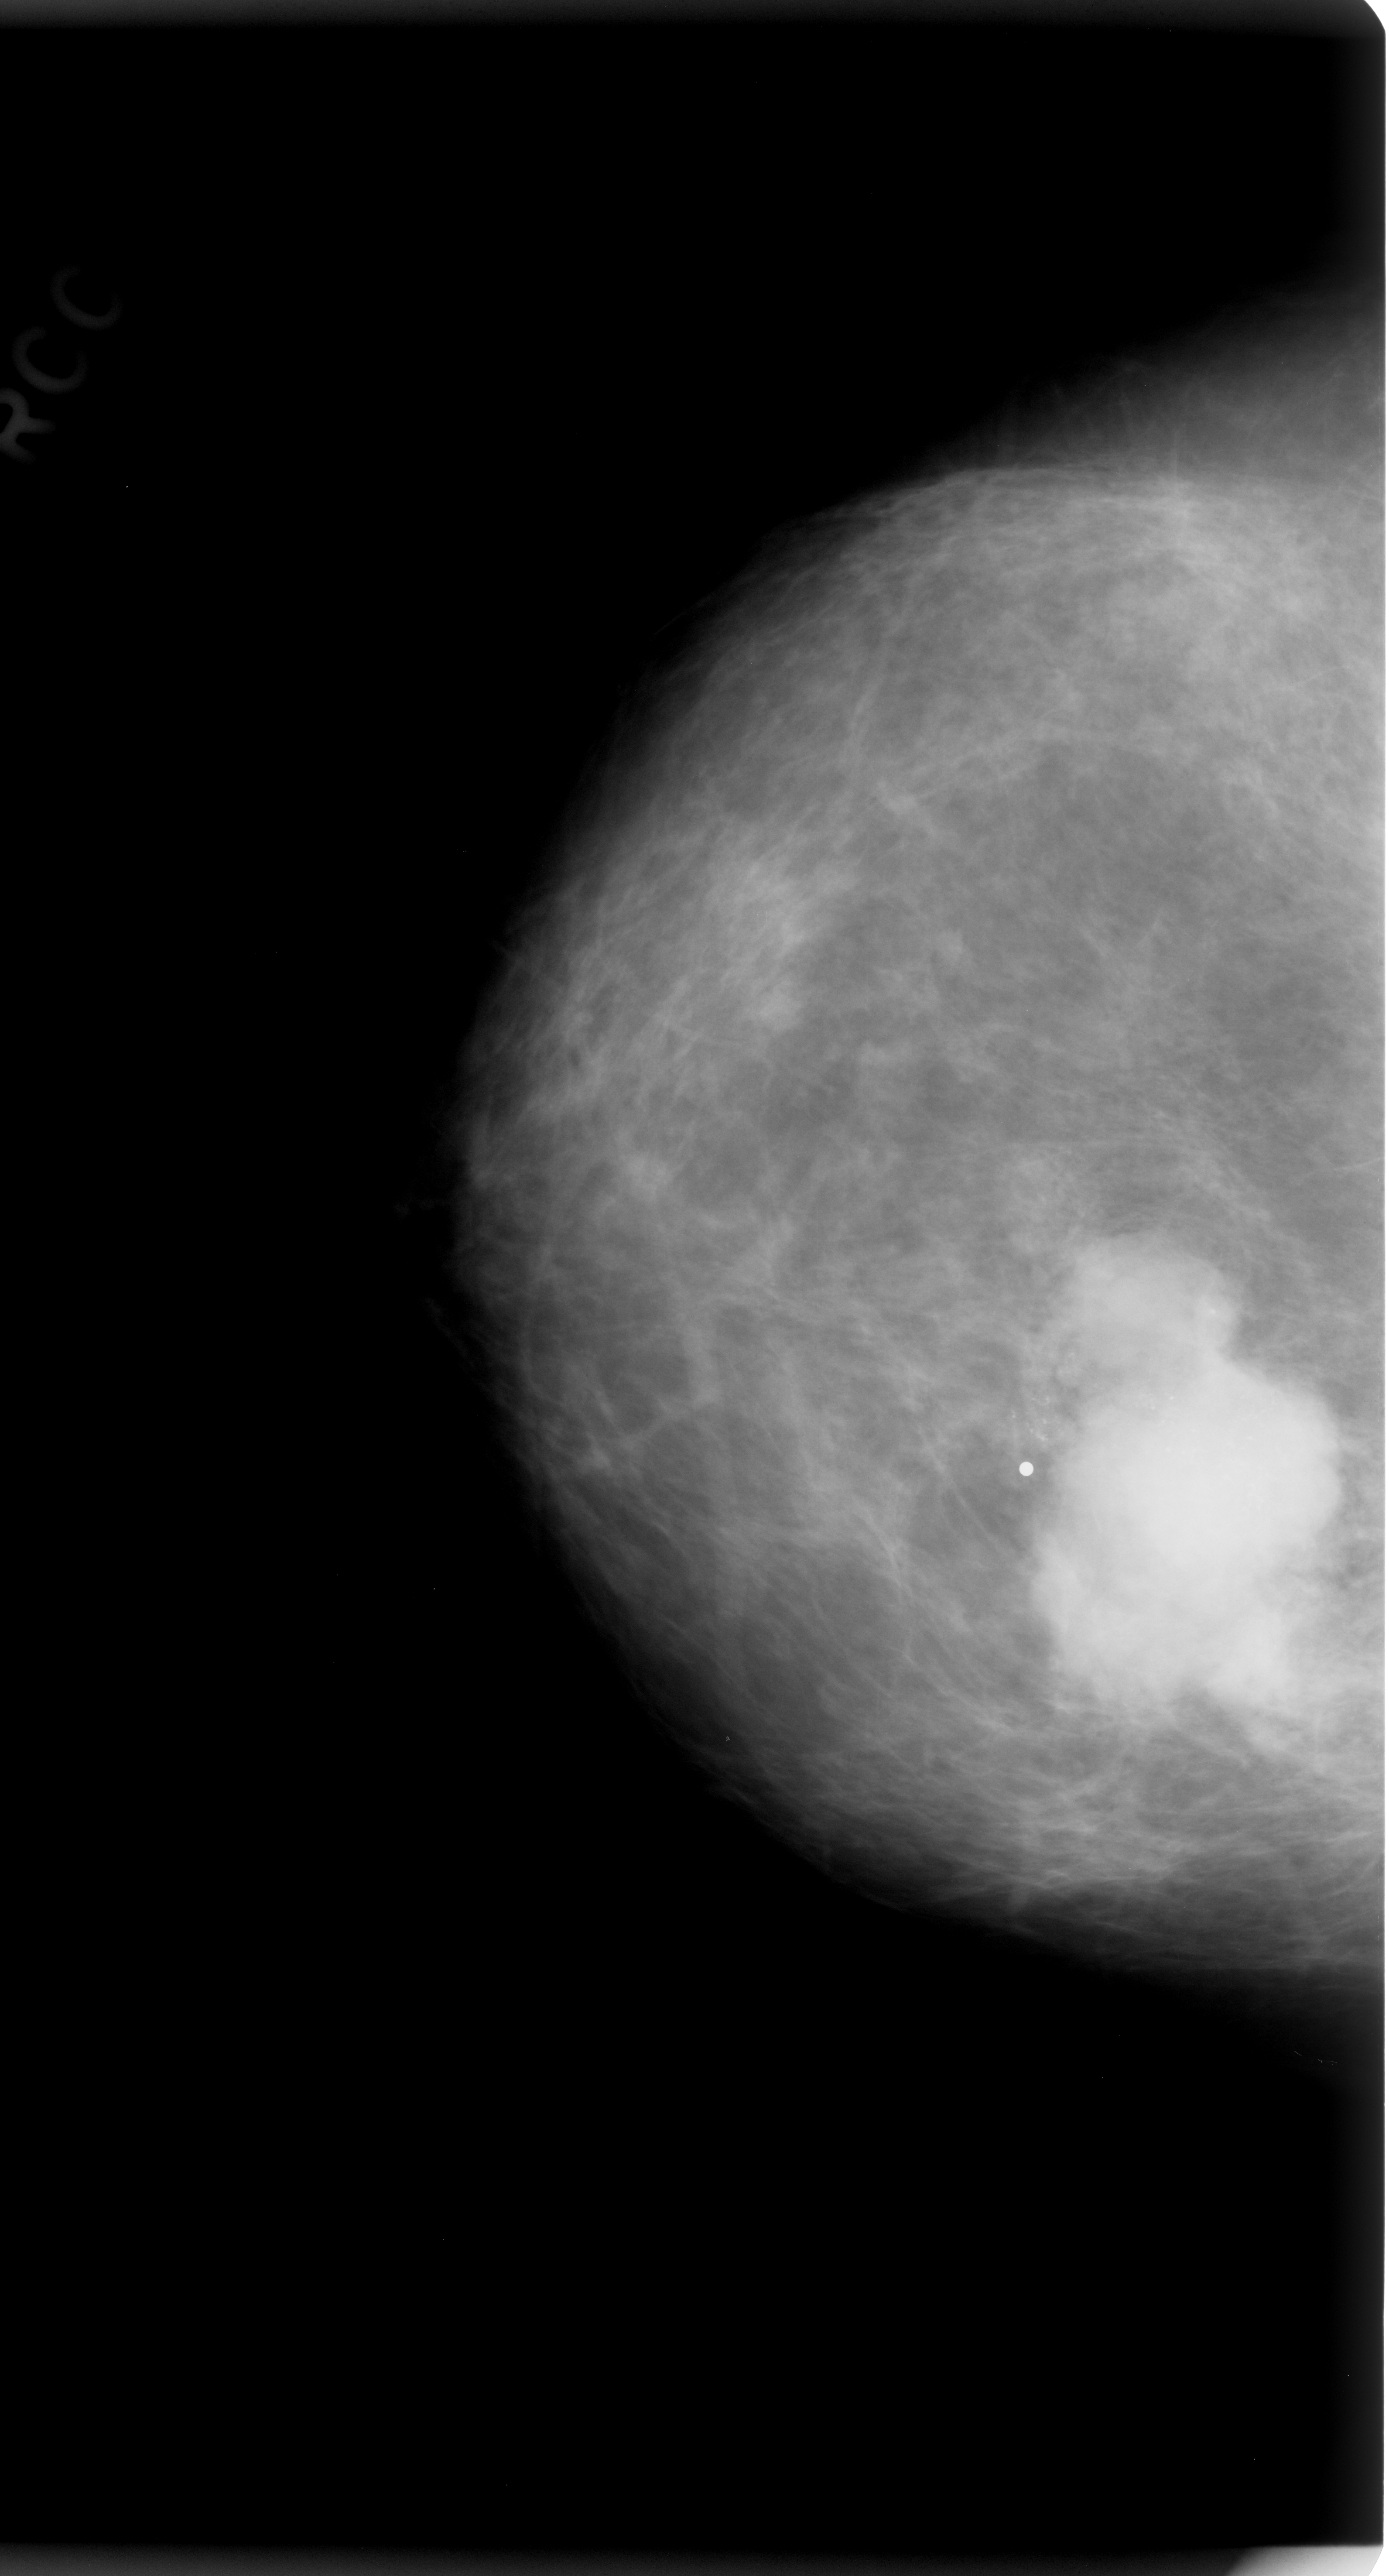
Mammogram (digitized film), right breast, CC view, breast composition: almost entirely fatty (BI-RADS density category 1 of 4).
- Calcifications, morphology pleomorphic, distribution clustered; BI-RADS assessment category 5; pathology (as recorded): malignant.